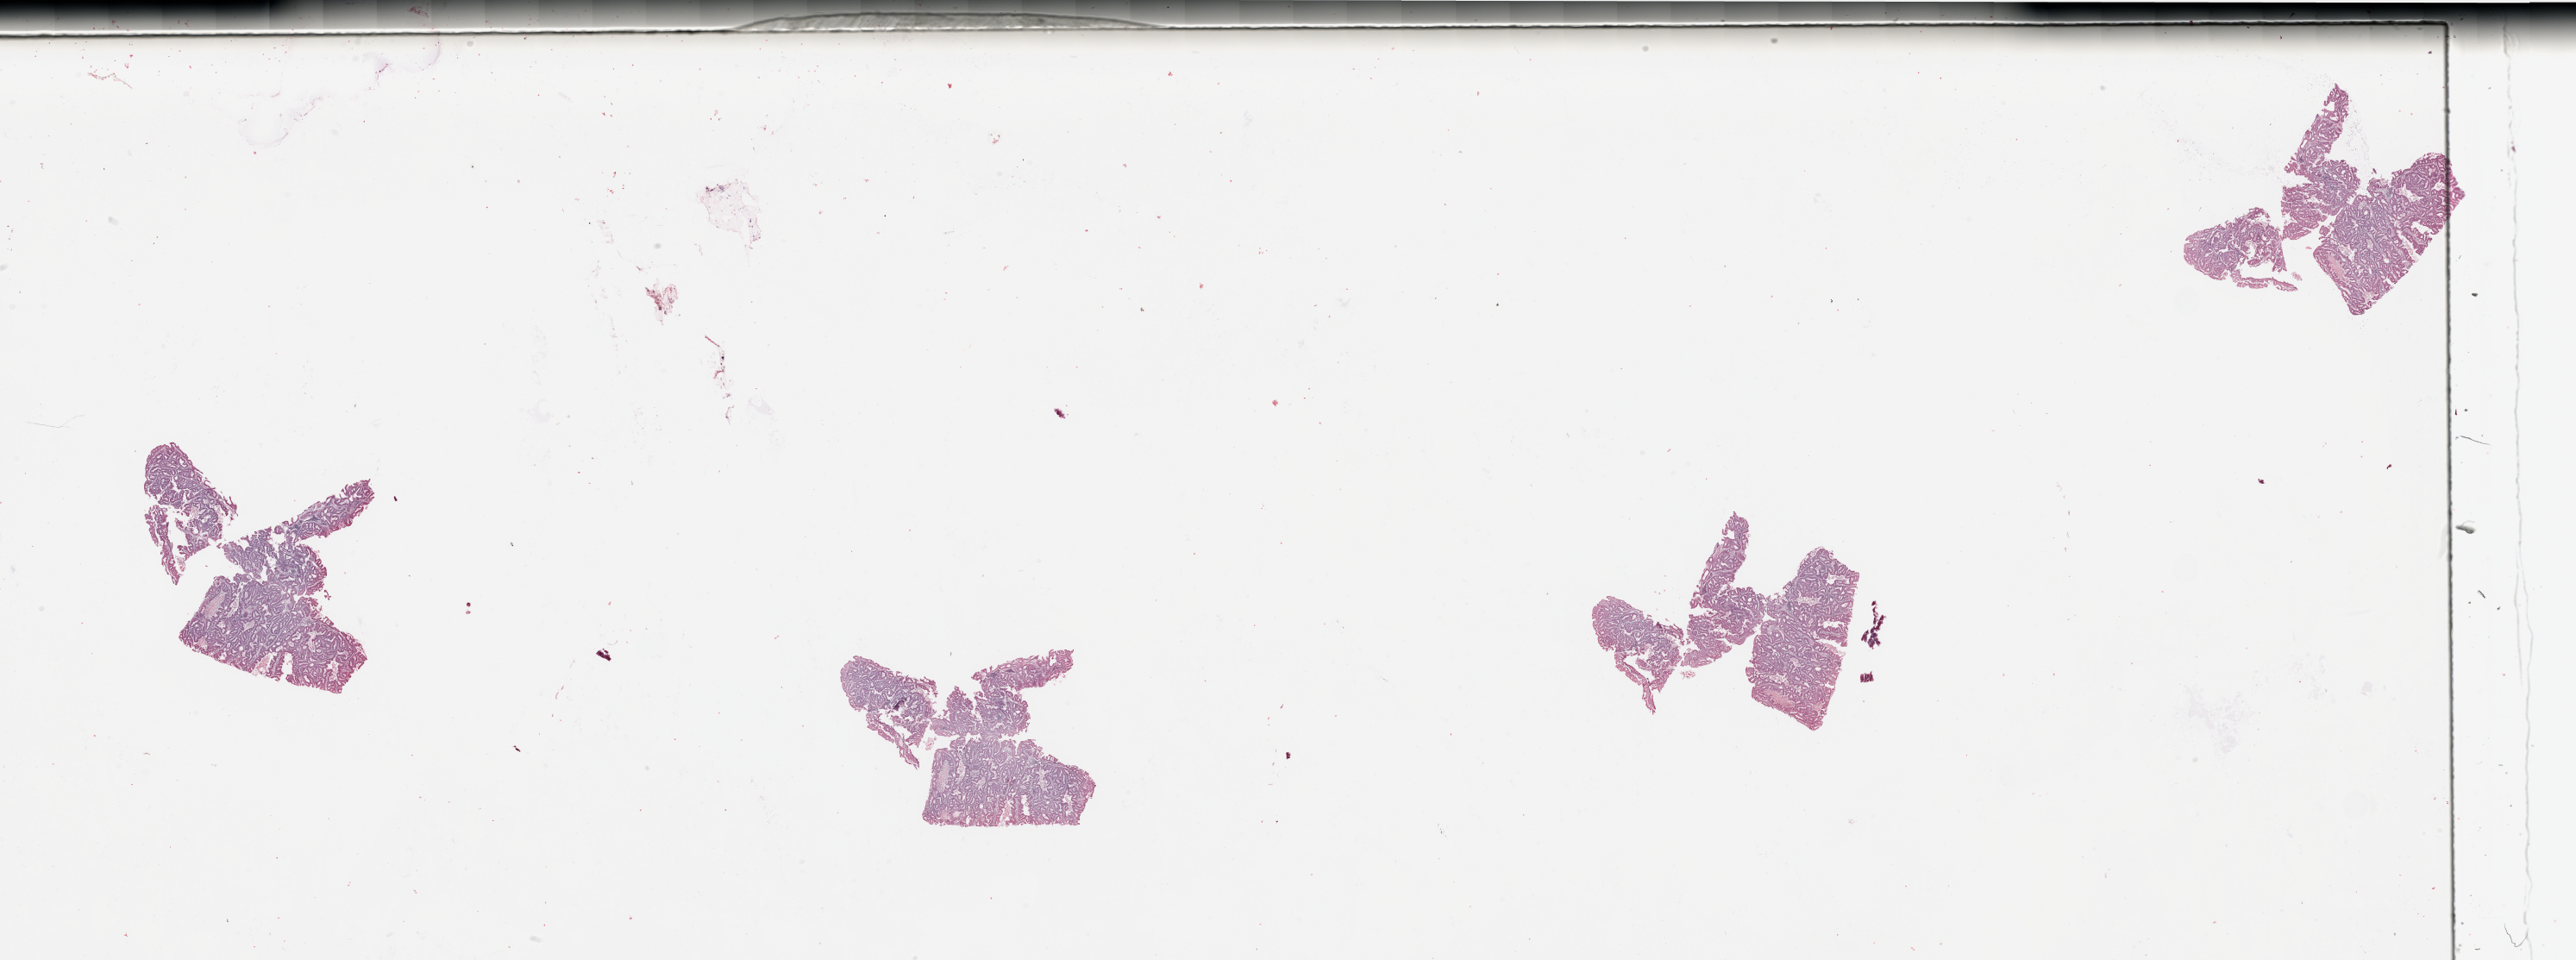
H&E-stained whole-slide image, whole scanned area (about 47.3 x 17.6 mm, acquisition: 20x scan) shown as a low-resolution overview; tumour tissue sample, sampled site: uterus. Patient: female, age 65 years. Histologic grade: G2 (moderately differentiated). Composition of this section per pathologist review: tumour nuclei 85%, necrosis 10%.
AJCC pathologic stage: III. Histologic diagnosis: Endometrioid adenocarcinoma, NOS. Primary tumour site (as recorded): anterior endometrium.